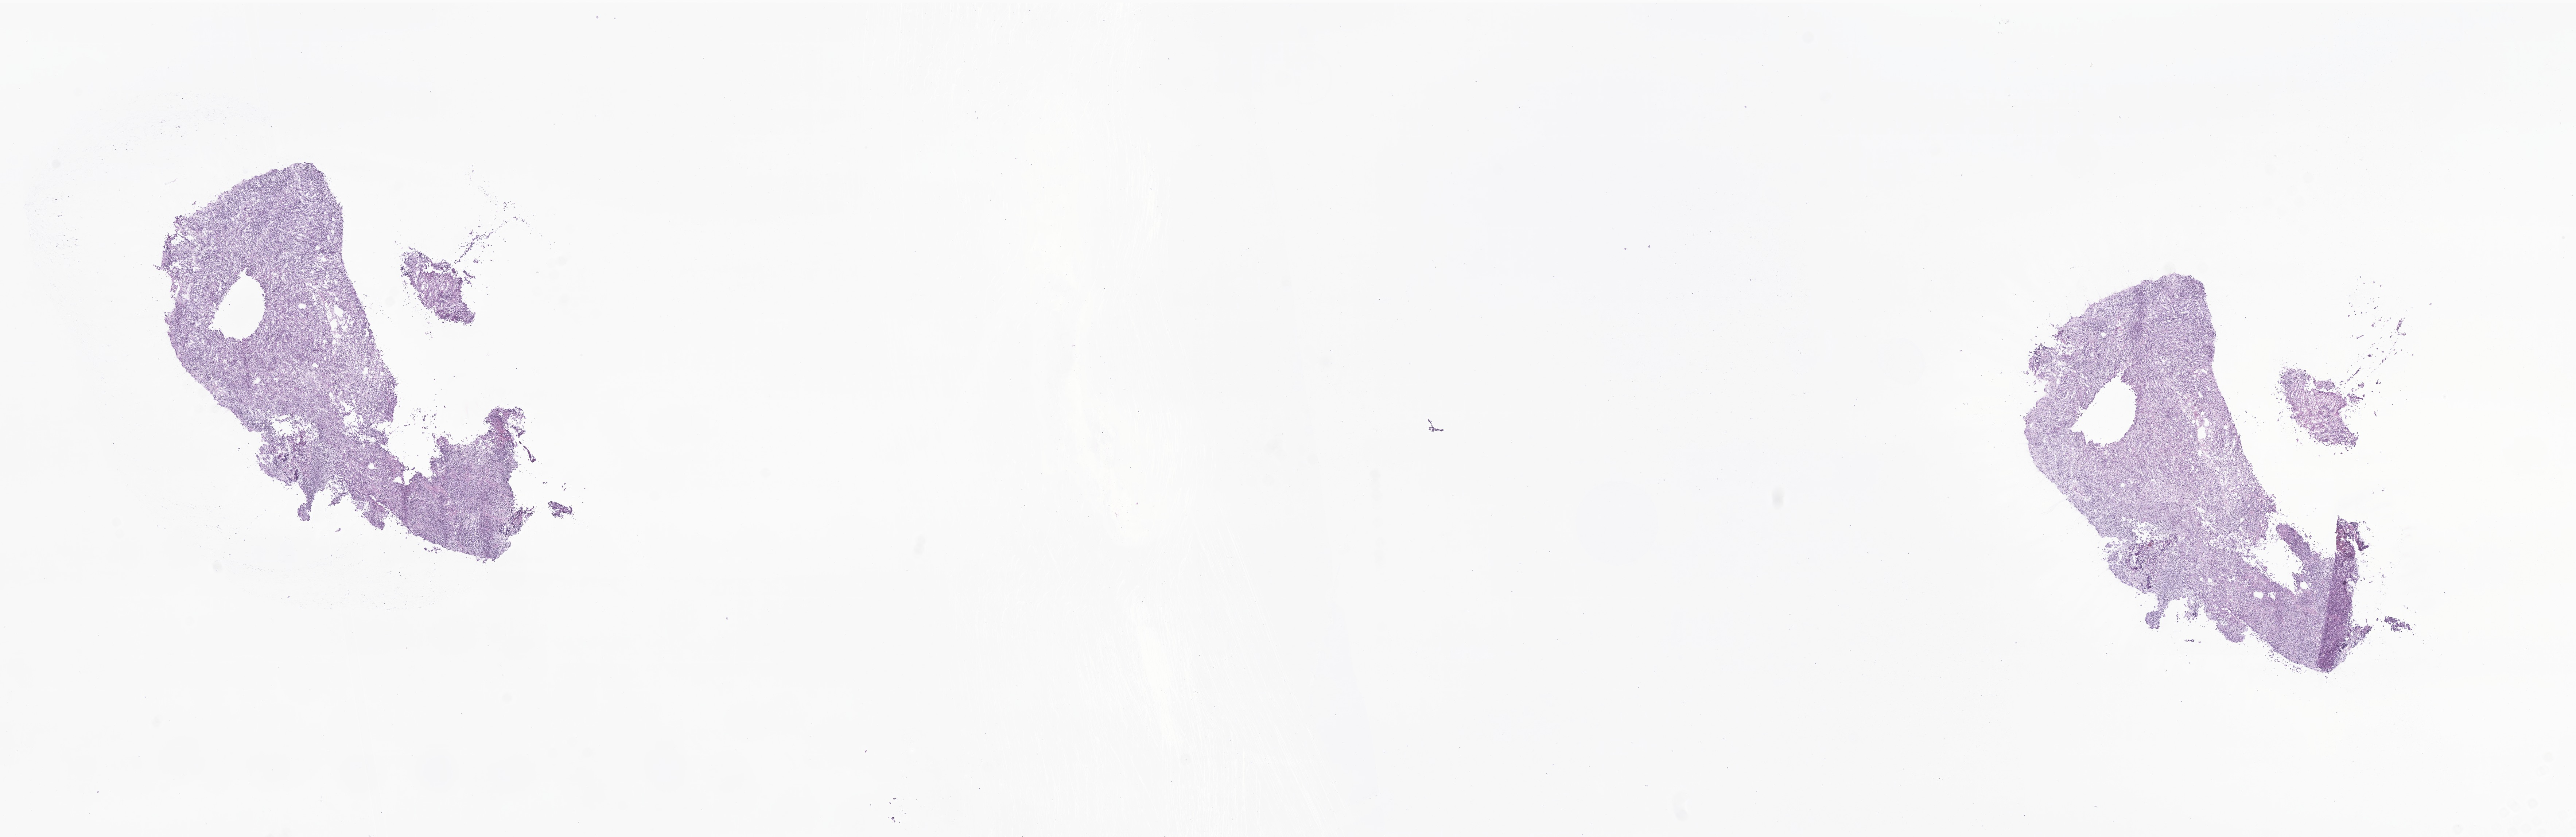
Digitized hematoxylin and eosin (H&E)-stained section of tumor tissue from the brain — shown as a low-resolution overview of the whole scanned area (about 29.8 x 9.7 mm), frozen section. Patient: male, age 71 months (5 years 11 months).
- diagnosis: Medulloblastoma, NOS